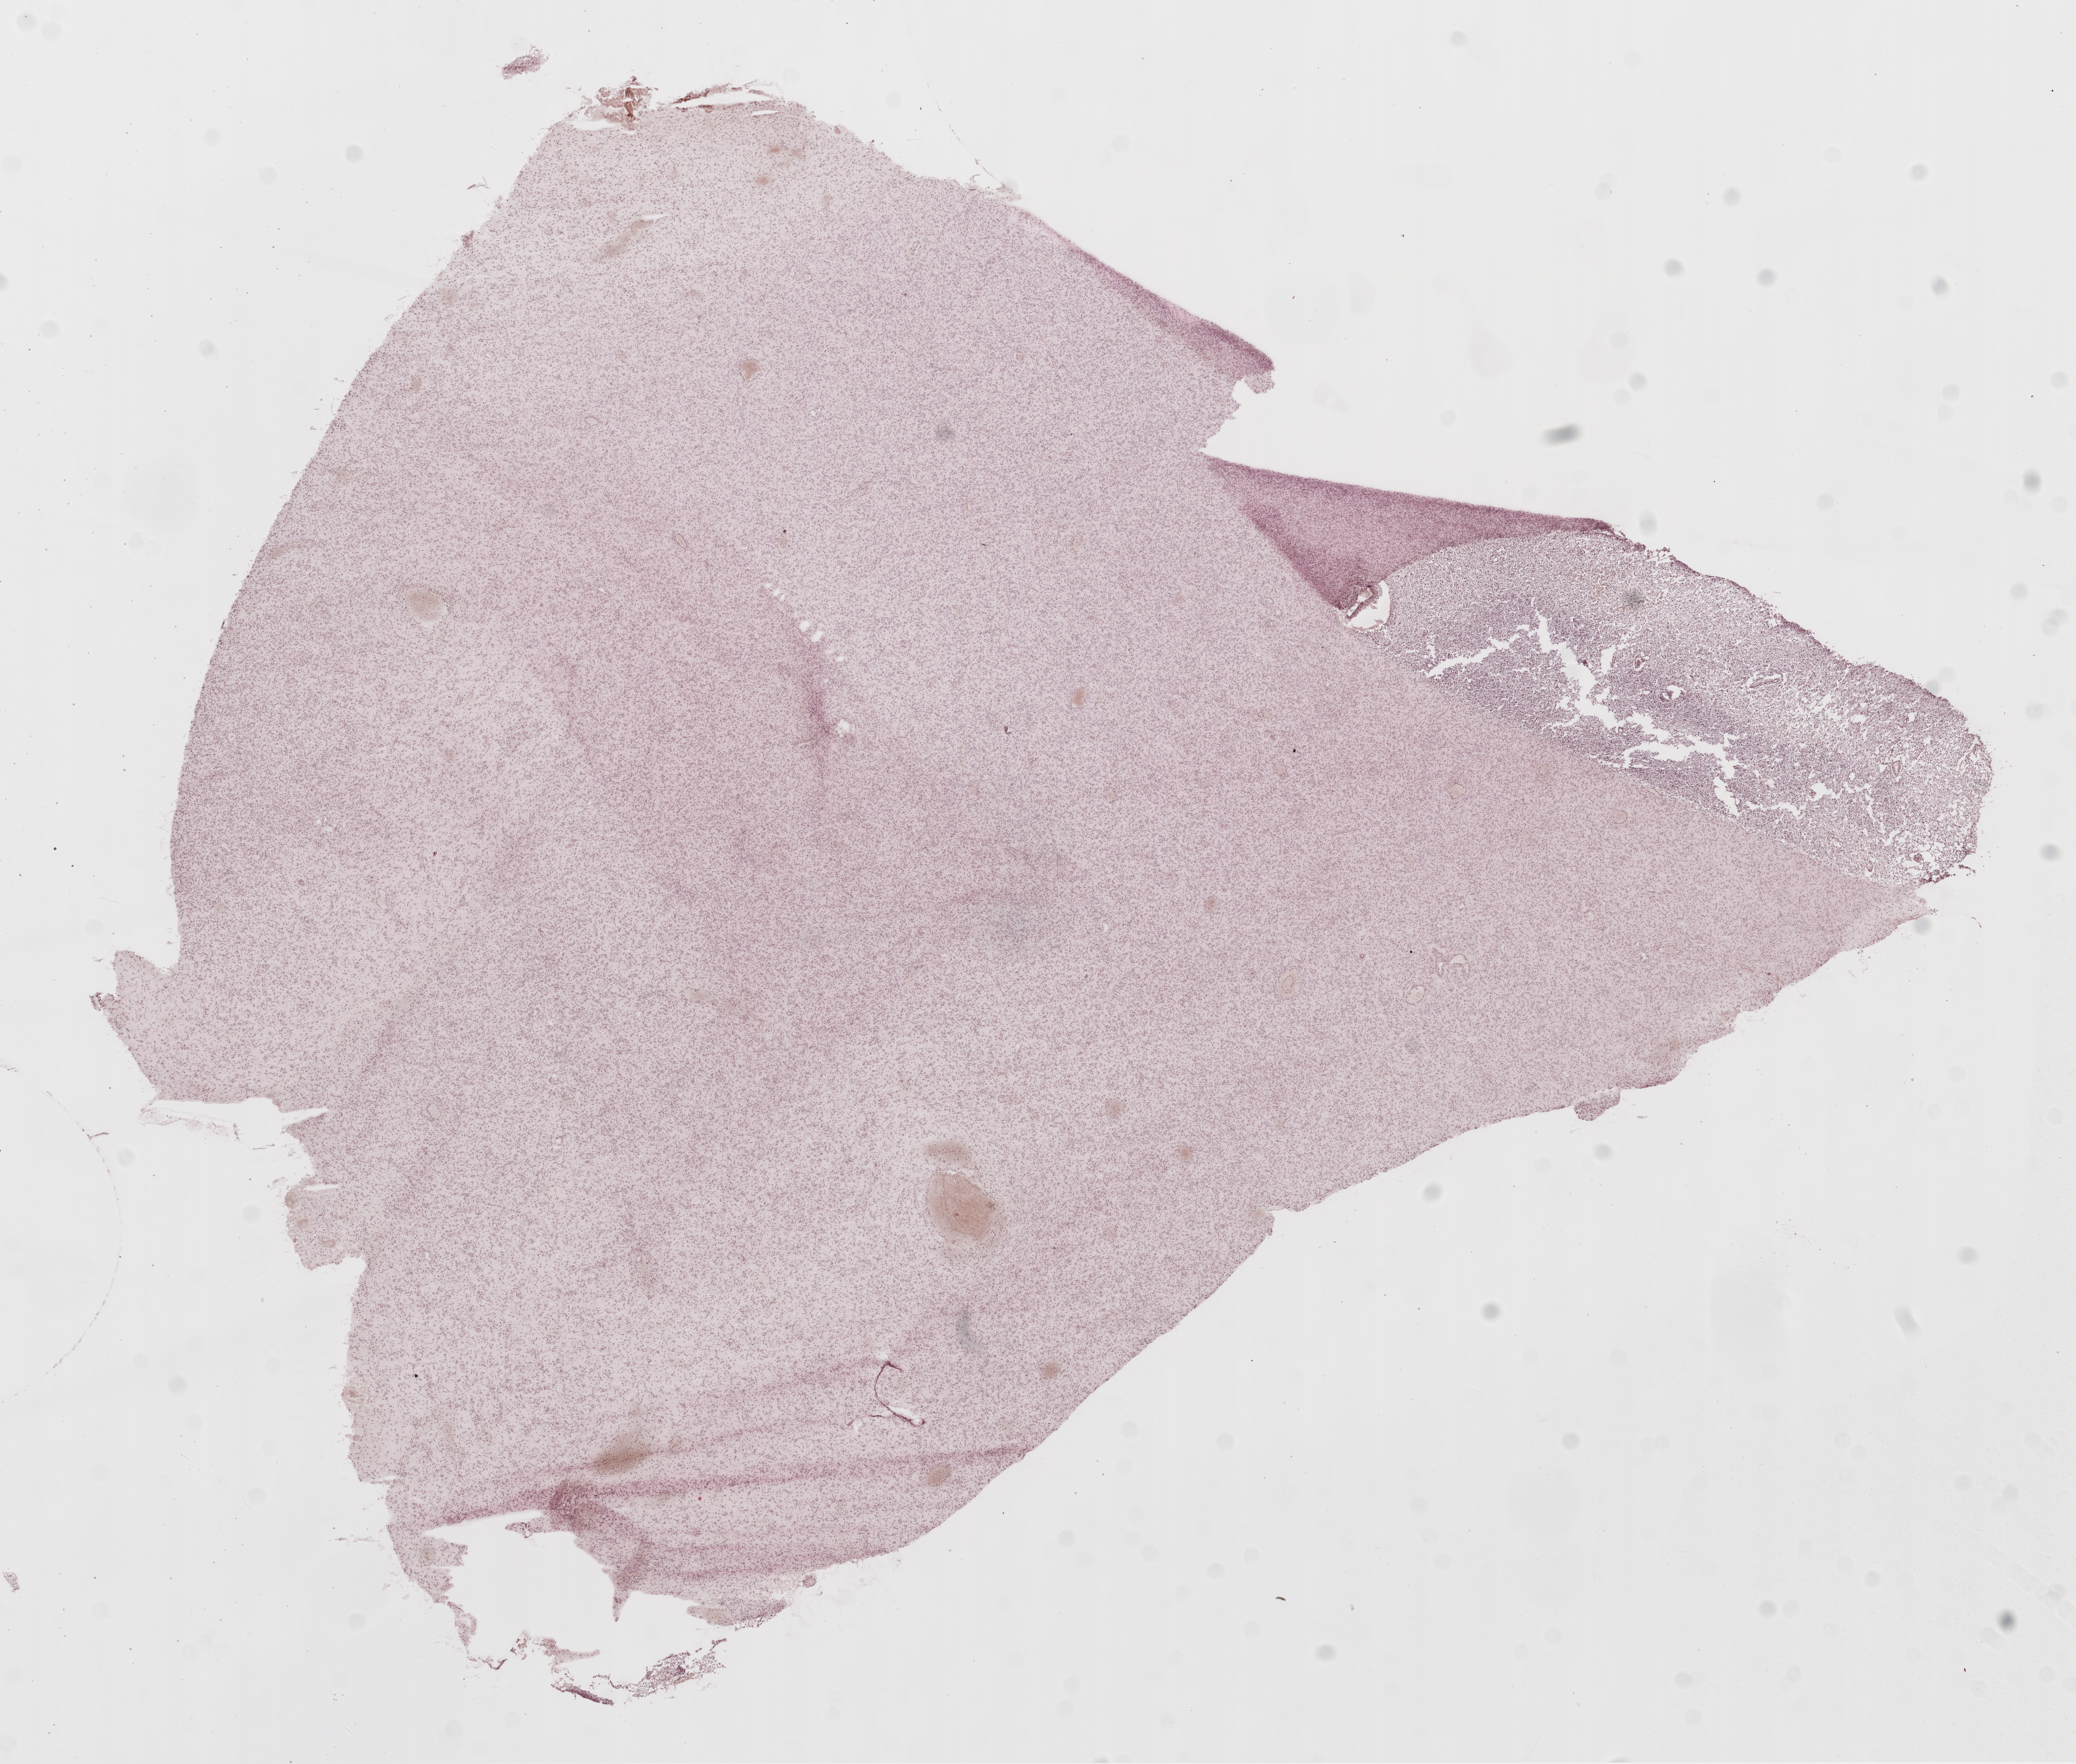
H&E whole-slide image, shown as a low-resolution overview of the whole scanned area (about 14.5 x 12.3 mm, slide scanned at 20x). Frozen section. Primary tumour sample from the brain. Male patient; age at initial diagnosis 60 years. Slide review estimates, as recorded: tumour cells 100%, tumour nuclei 100%, normal cells 0%, stromal cells 0%, necrosis 0%.
Pathologic diagnosis: Glioblastoma.